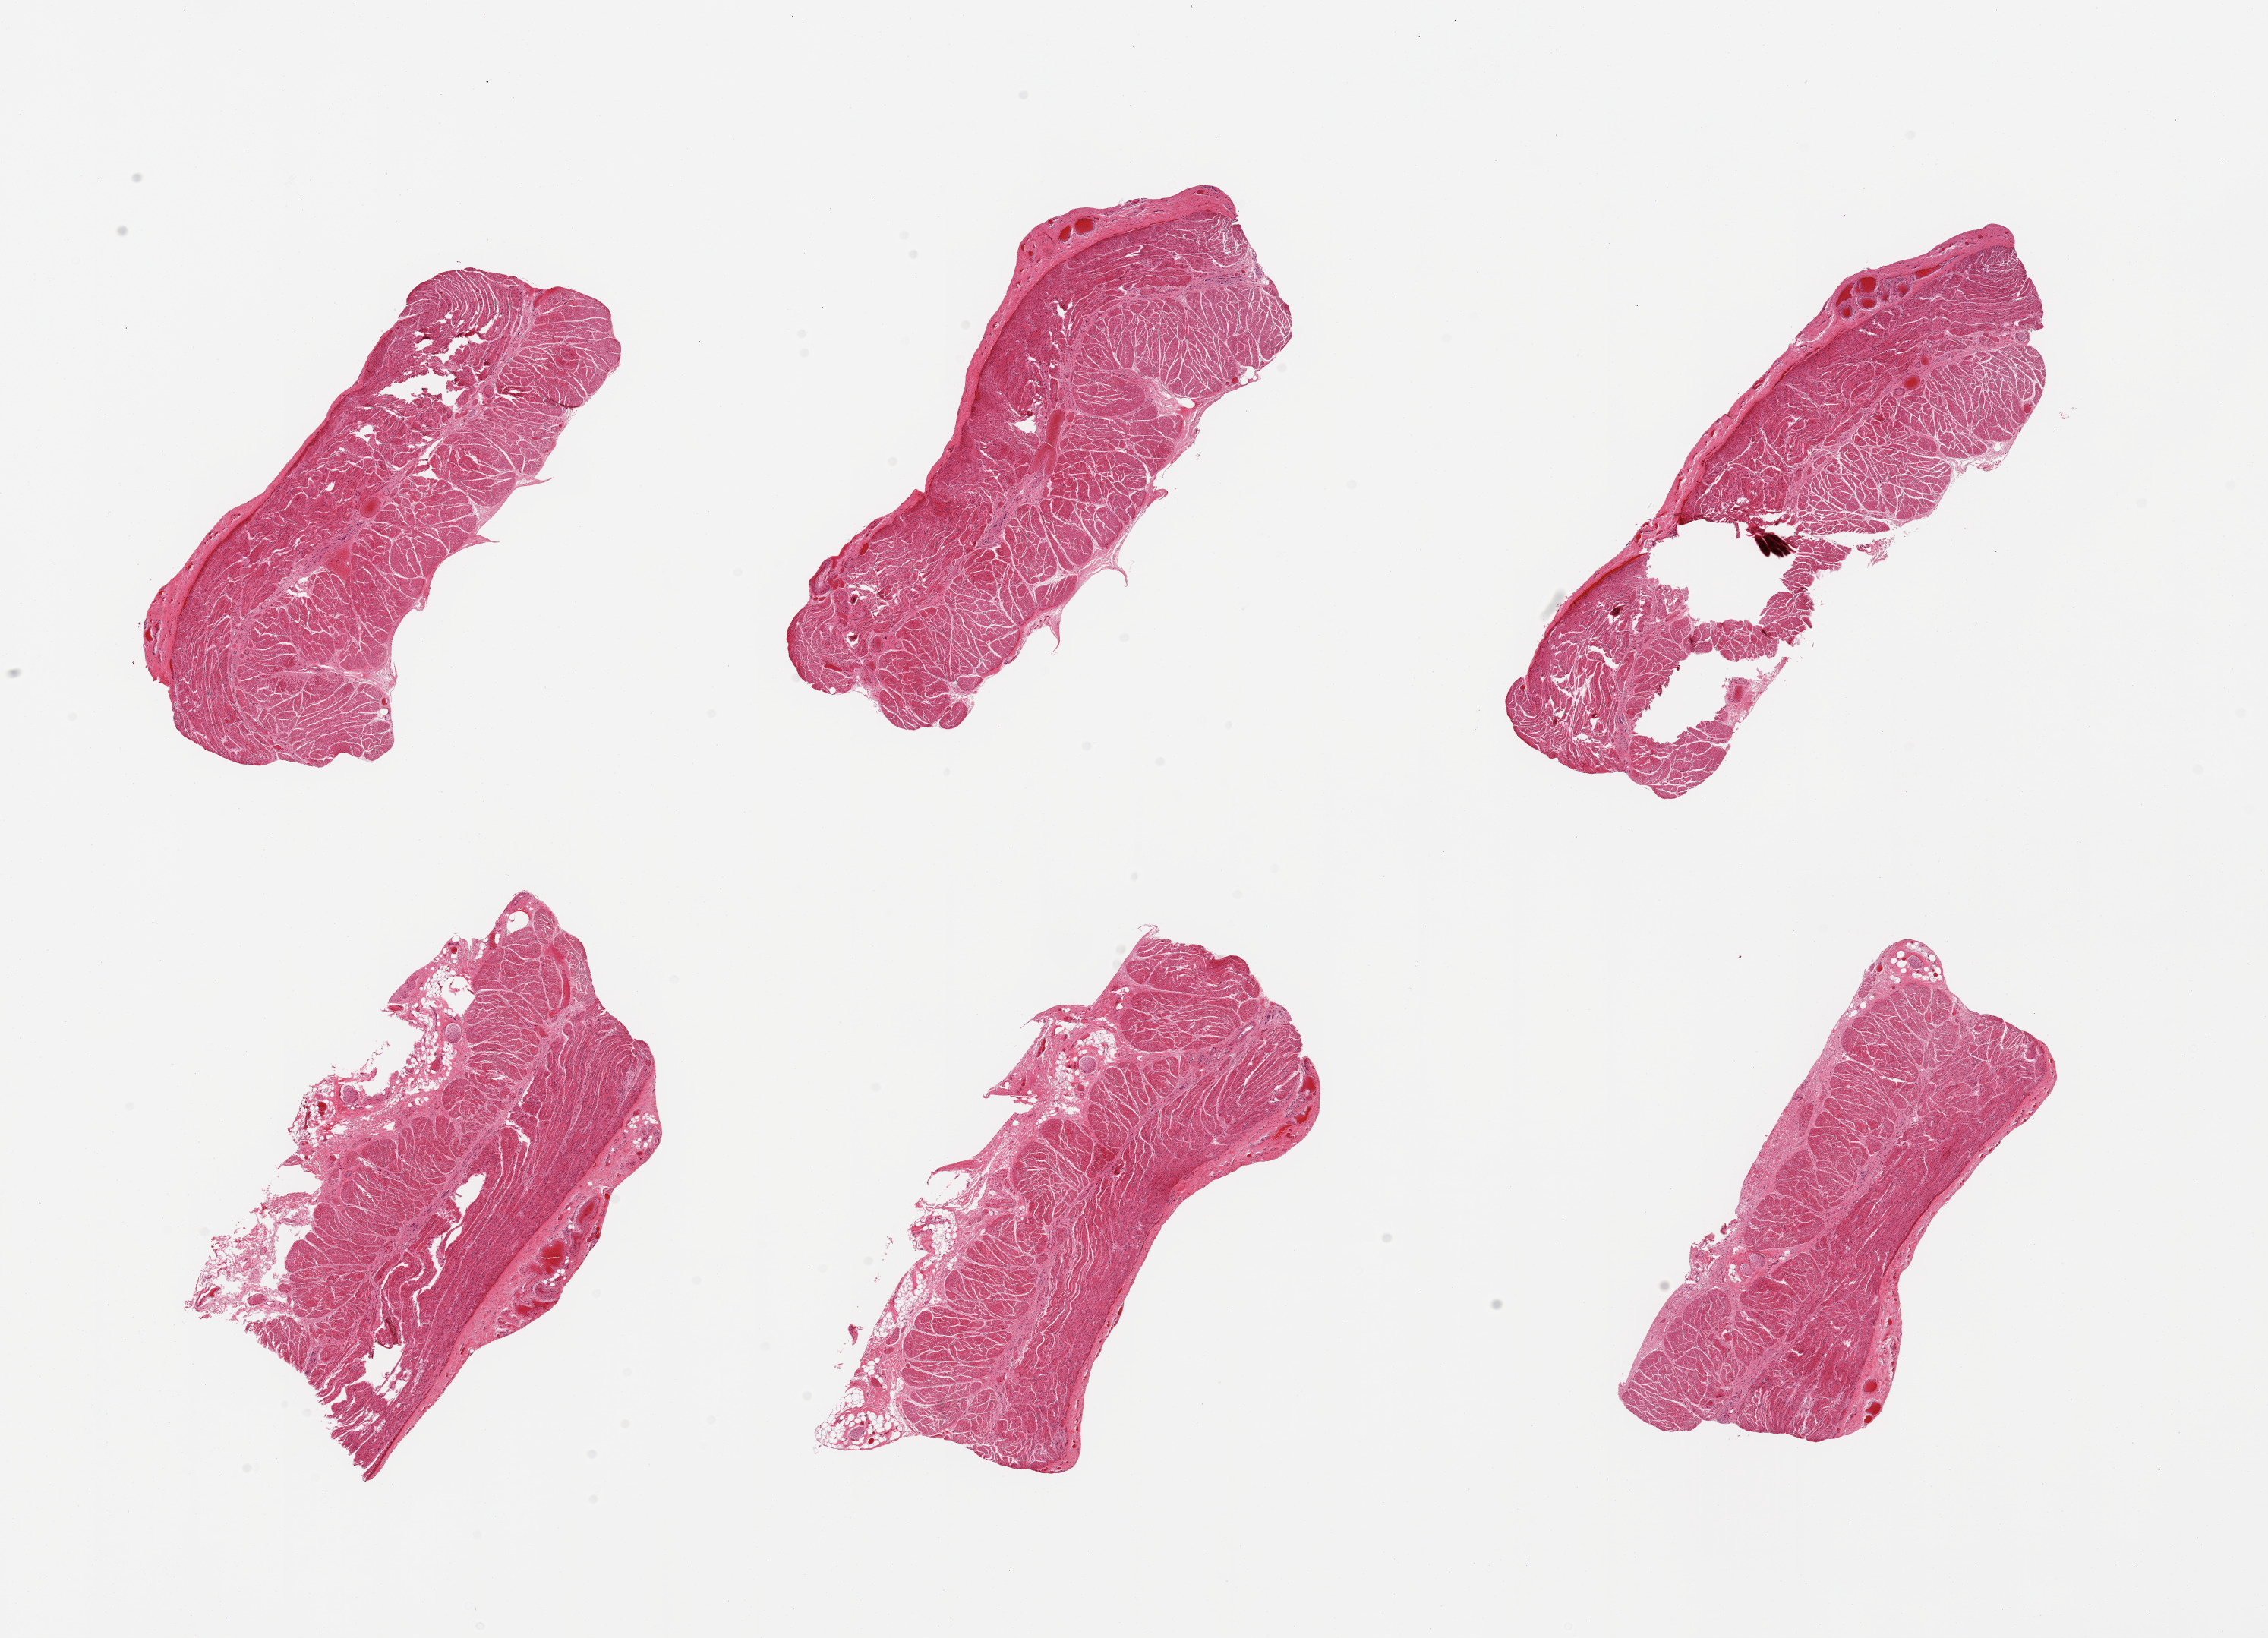
Digitized H&E-stained section, shown as a low-resolution overview of the whole scanned area (about 23.6 x 17.1 mm); PAXgene-fixed, paraffin-embedded tissue; target tissue: esophageal muscle; donor tissue sample. Donor sex: female.
Reviewer comment on this tissue sample: 6 pieces; 2 of 6 have fibrofatty submucosal stroma.